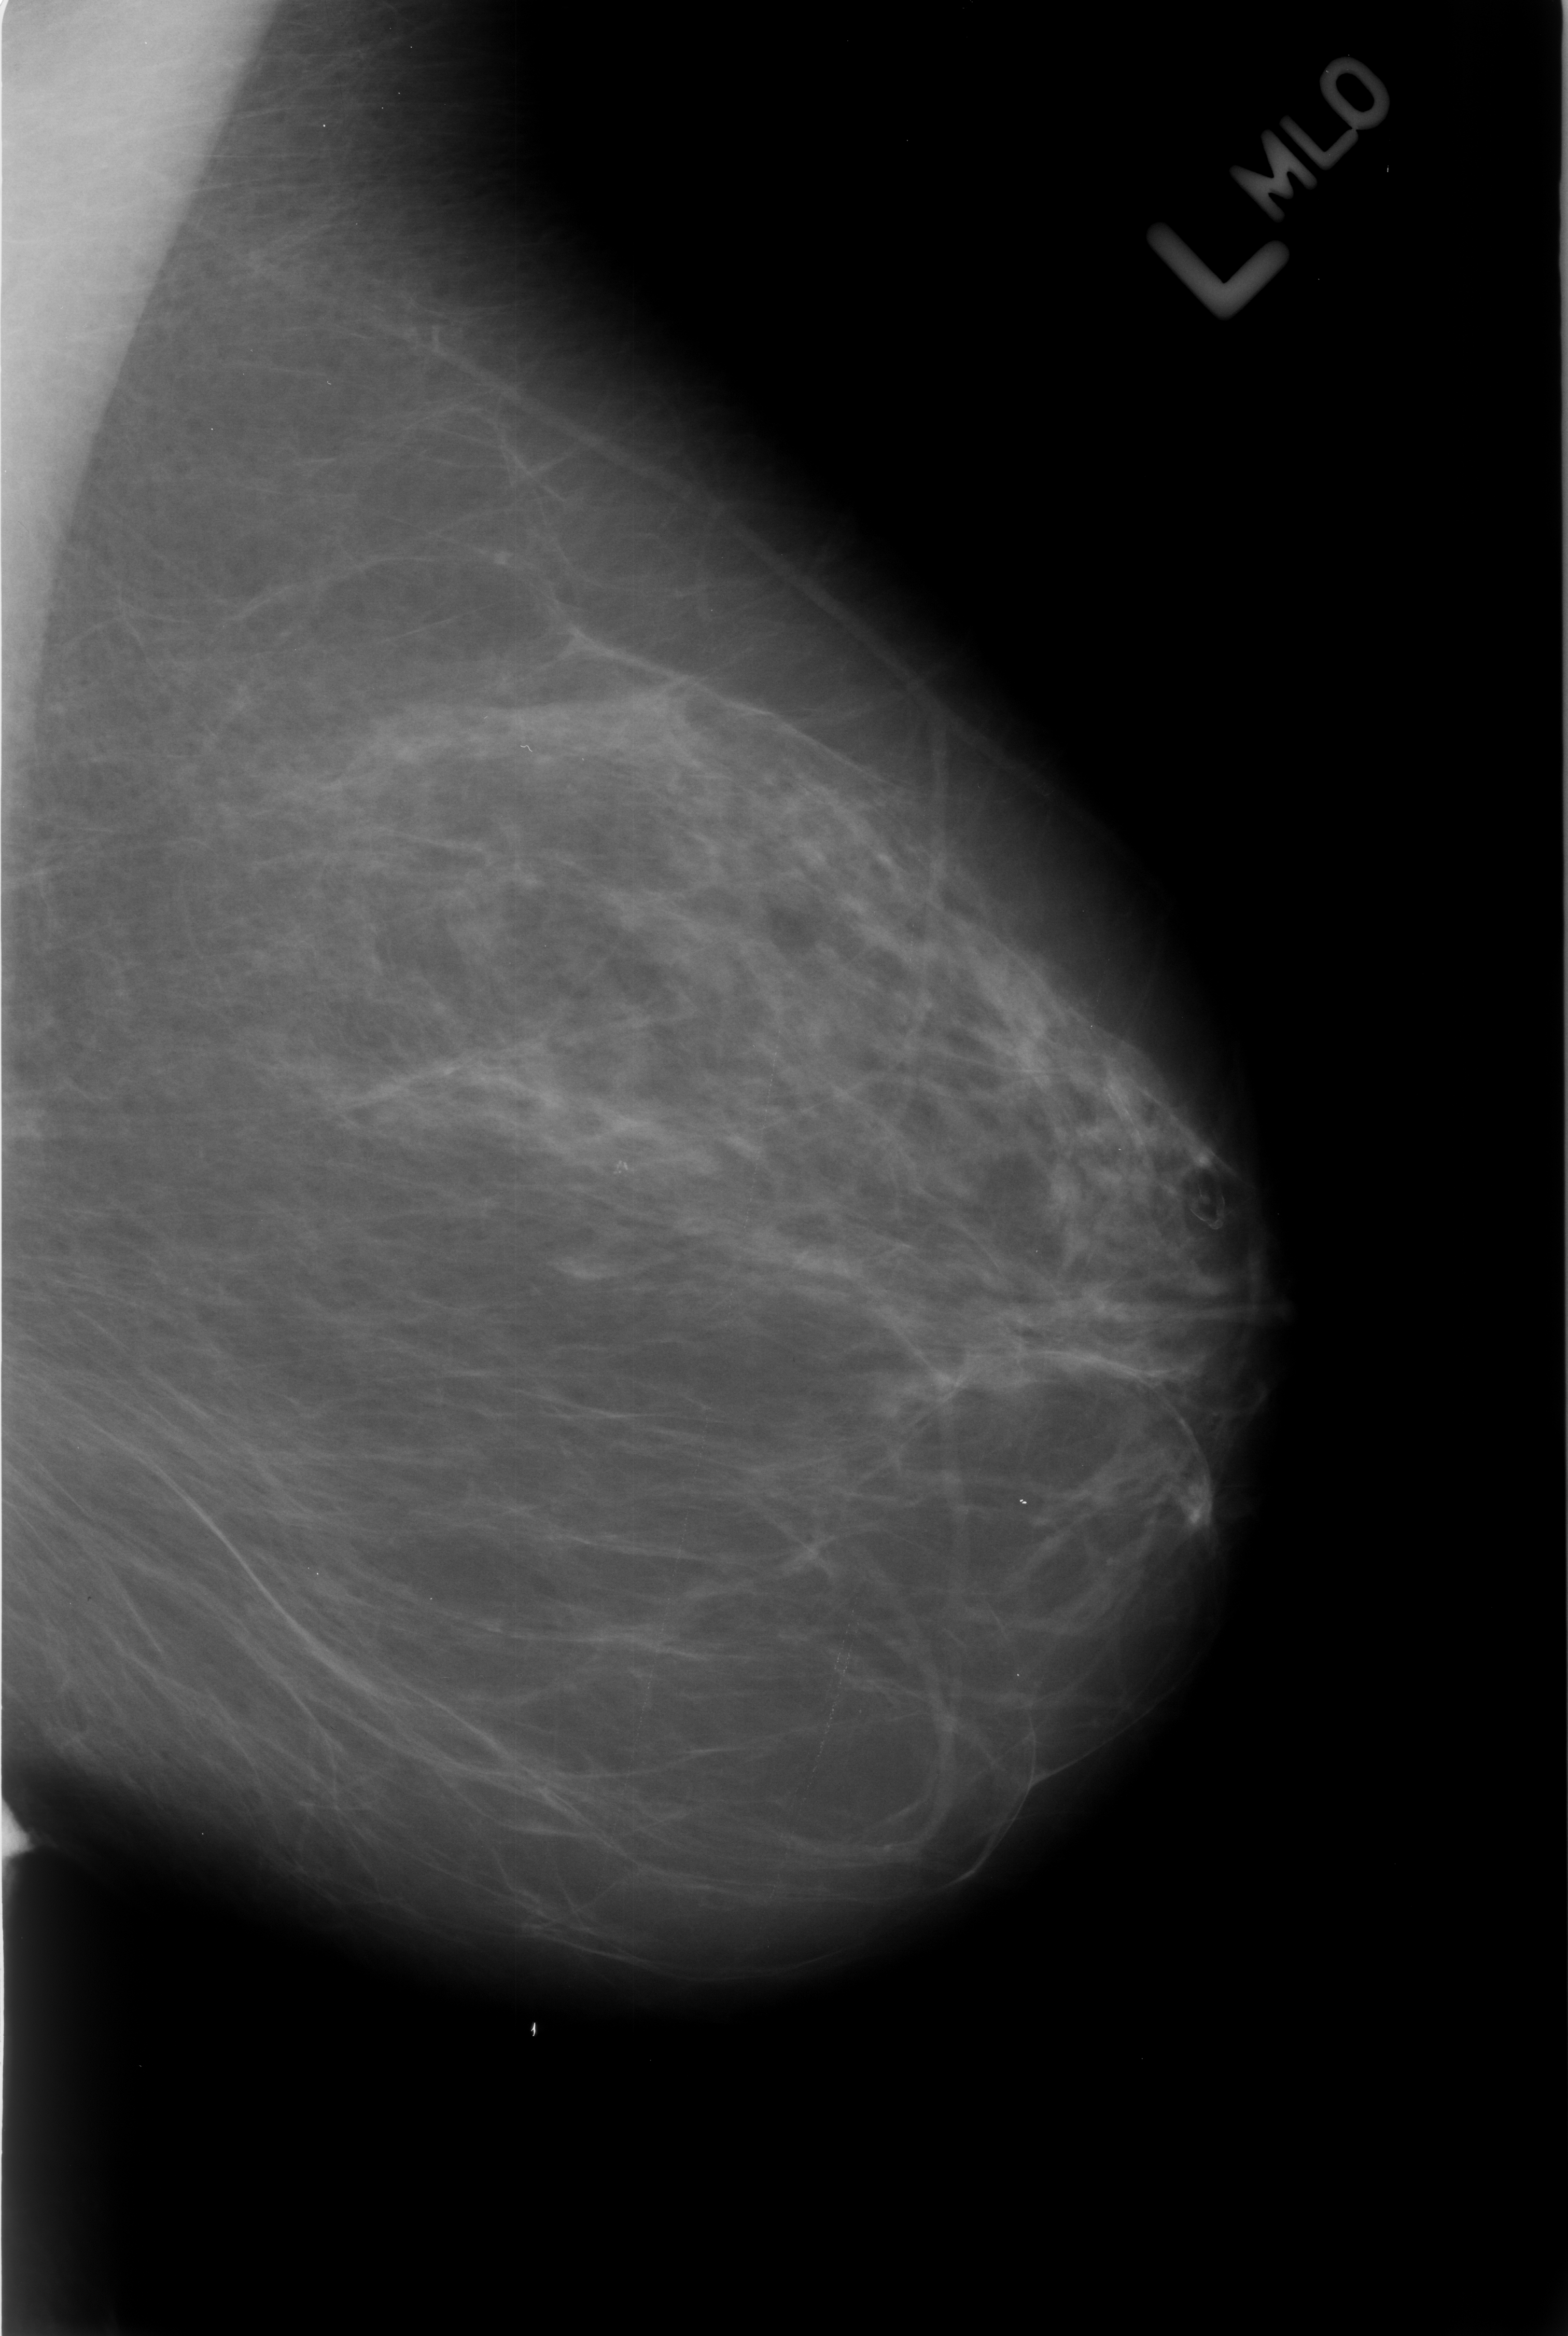
Scanned film-screen mammogram, left breast, mediolateral oblique (MLO) view, BI-RADS breast density category 2 (scale 1–4).
Abnormality record for this image: calcifications, morphology punctate / pleomorphic, distribution clustered; BI-RADS assessment category 4; pathology result (as recorded, not read from the image): benign.